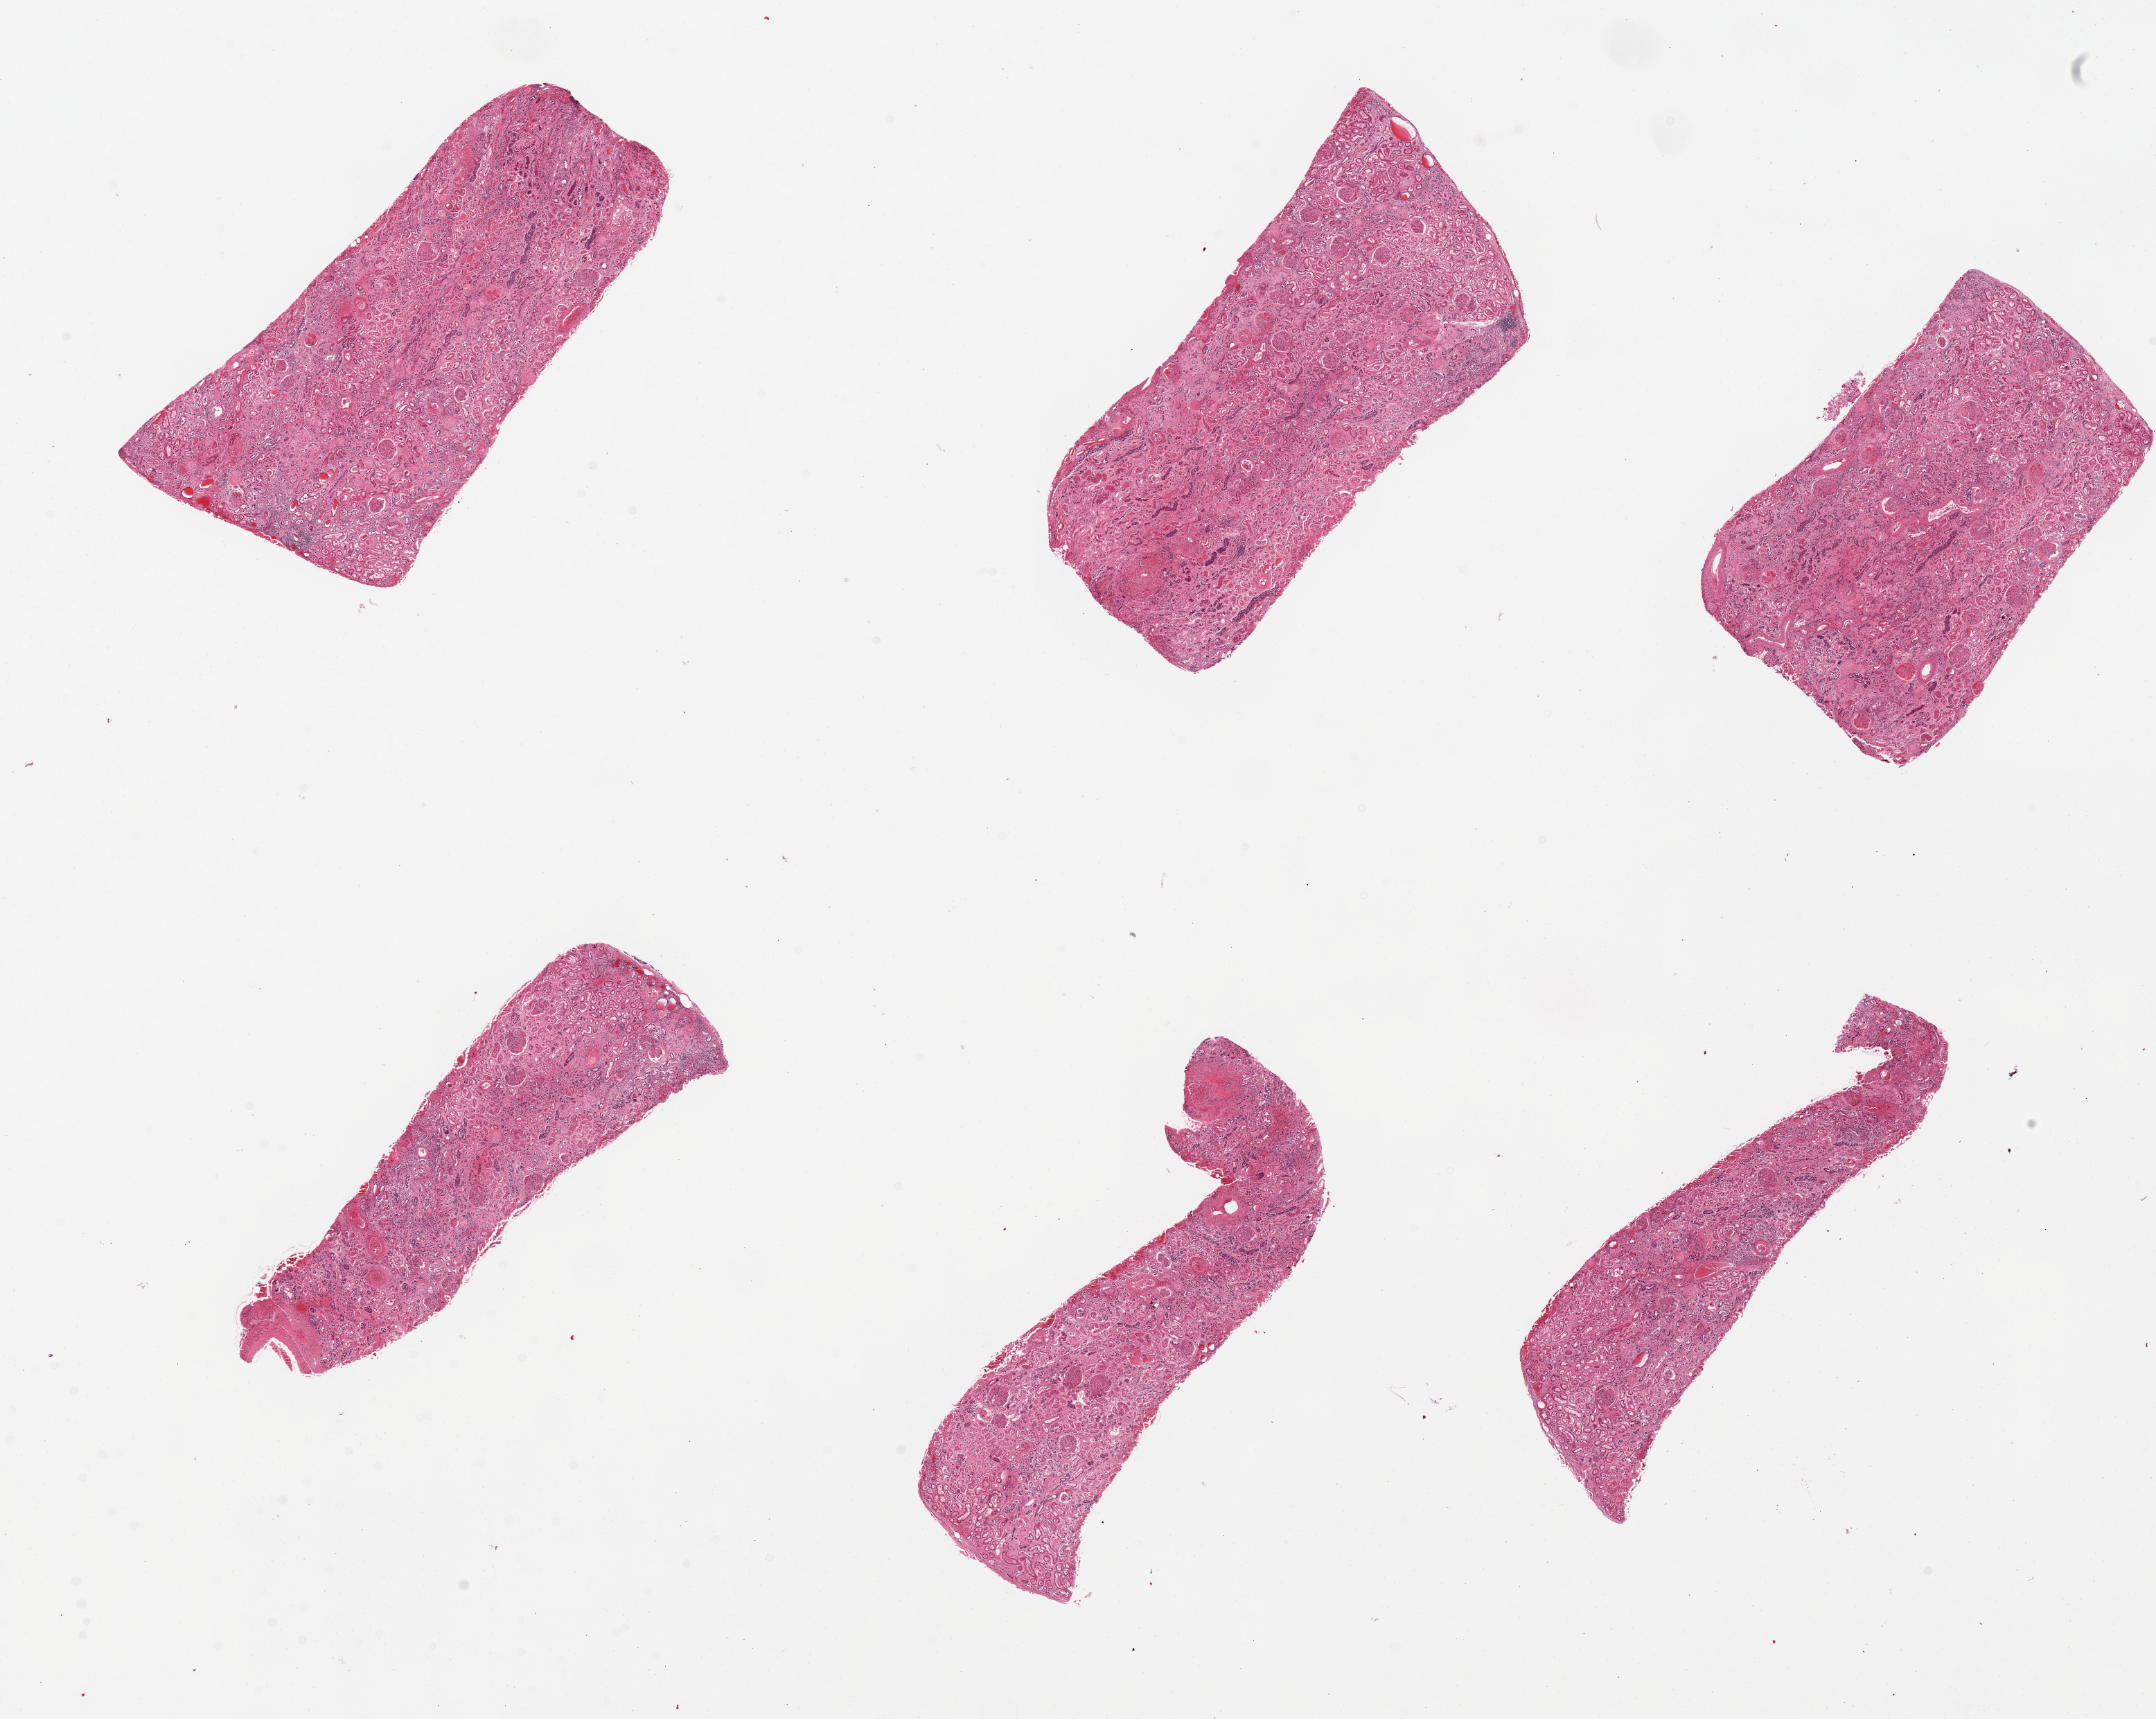
Whole-slide image, hematoxylin and eosin (H&E) stain — shown as a low-resolution overview of the whole scanned area (about 24.6 x 19.6 mm); PAXgene-fixed paraffin-embedded (PFPE) section; section of renal cortex (target tissue); donor tissue sample. Donor: male.
- pathologist's review note for this sample: 6 pieces; severe (diabetic) glomerulosclerosis